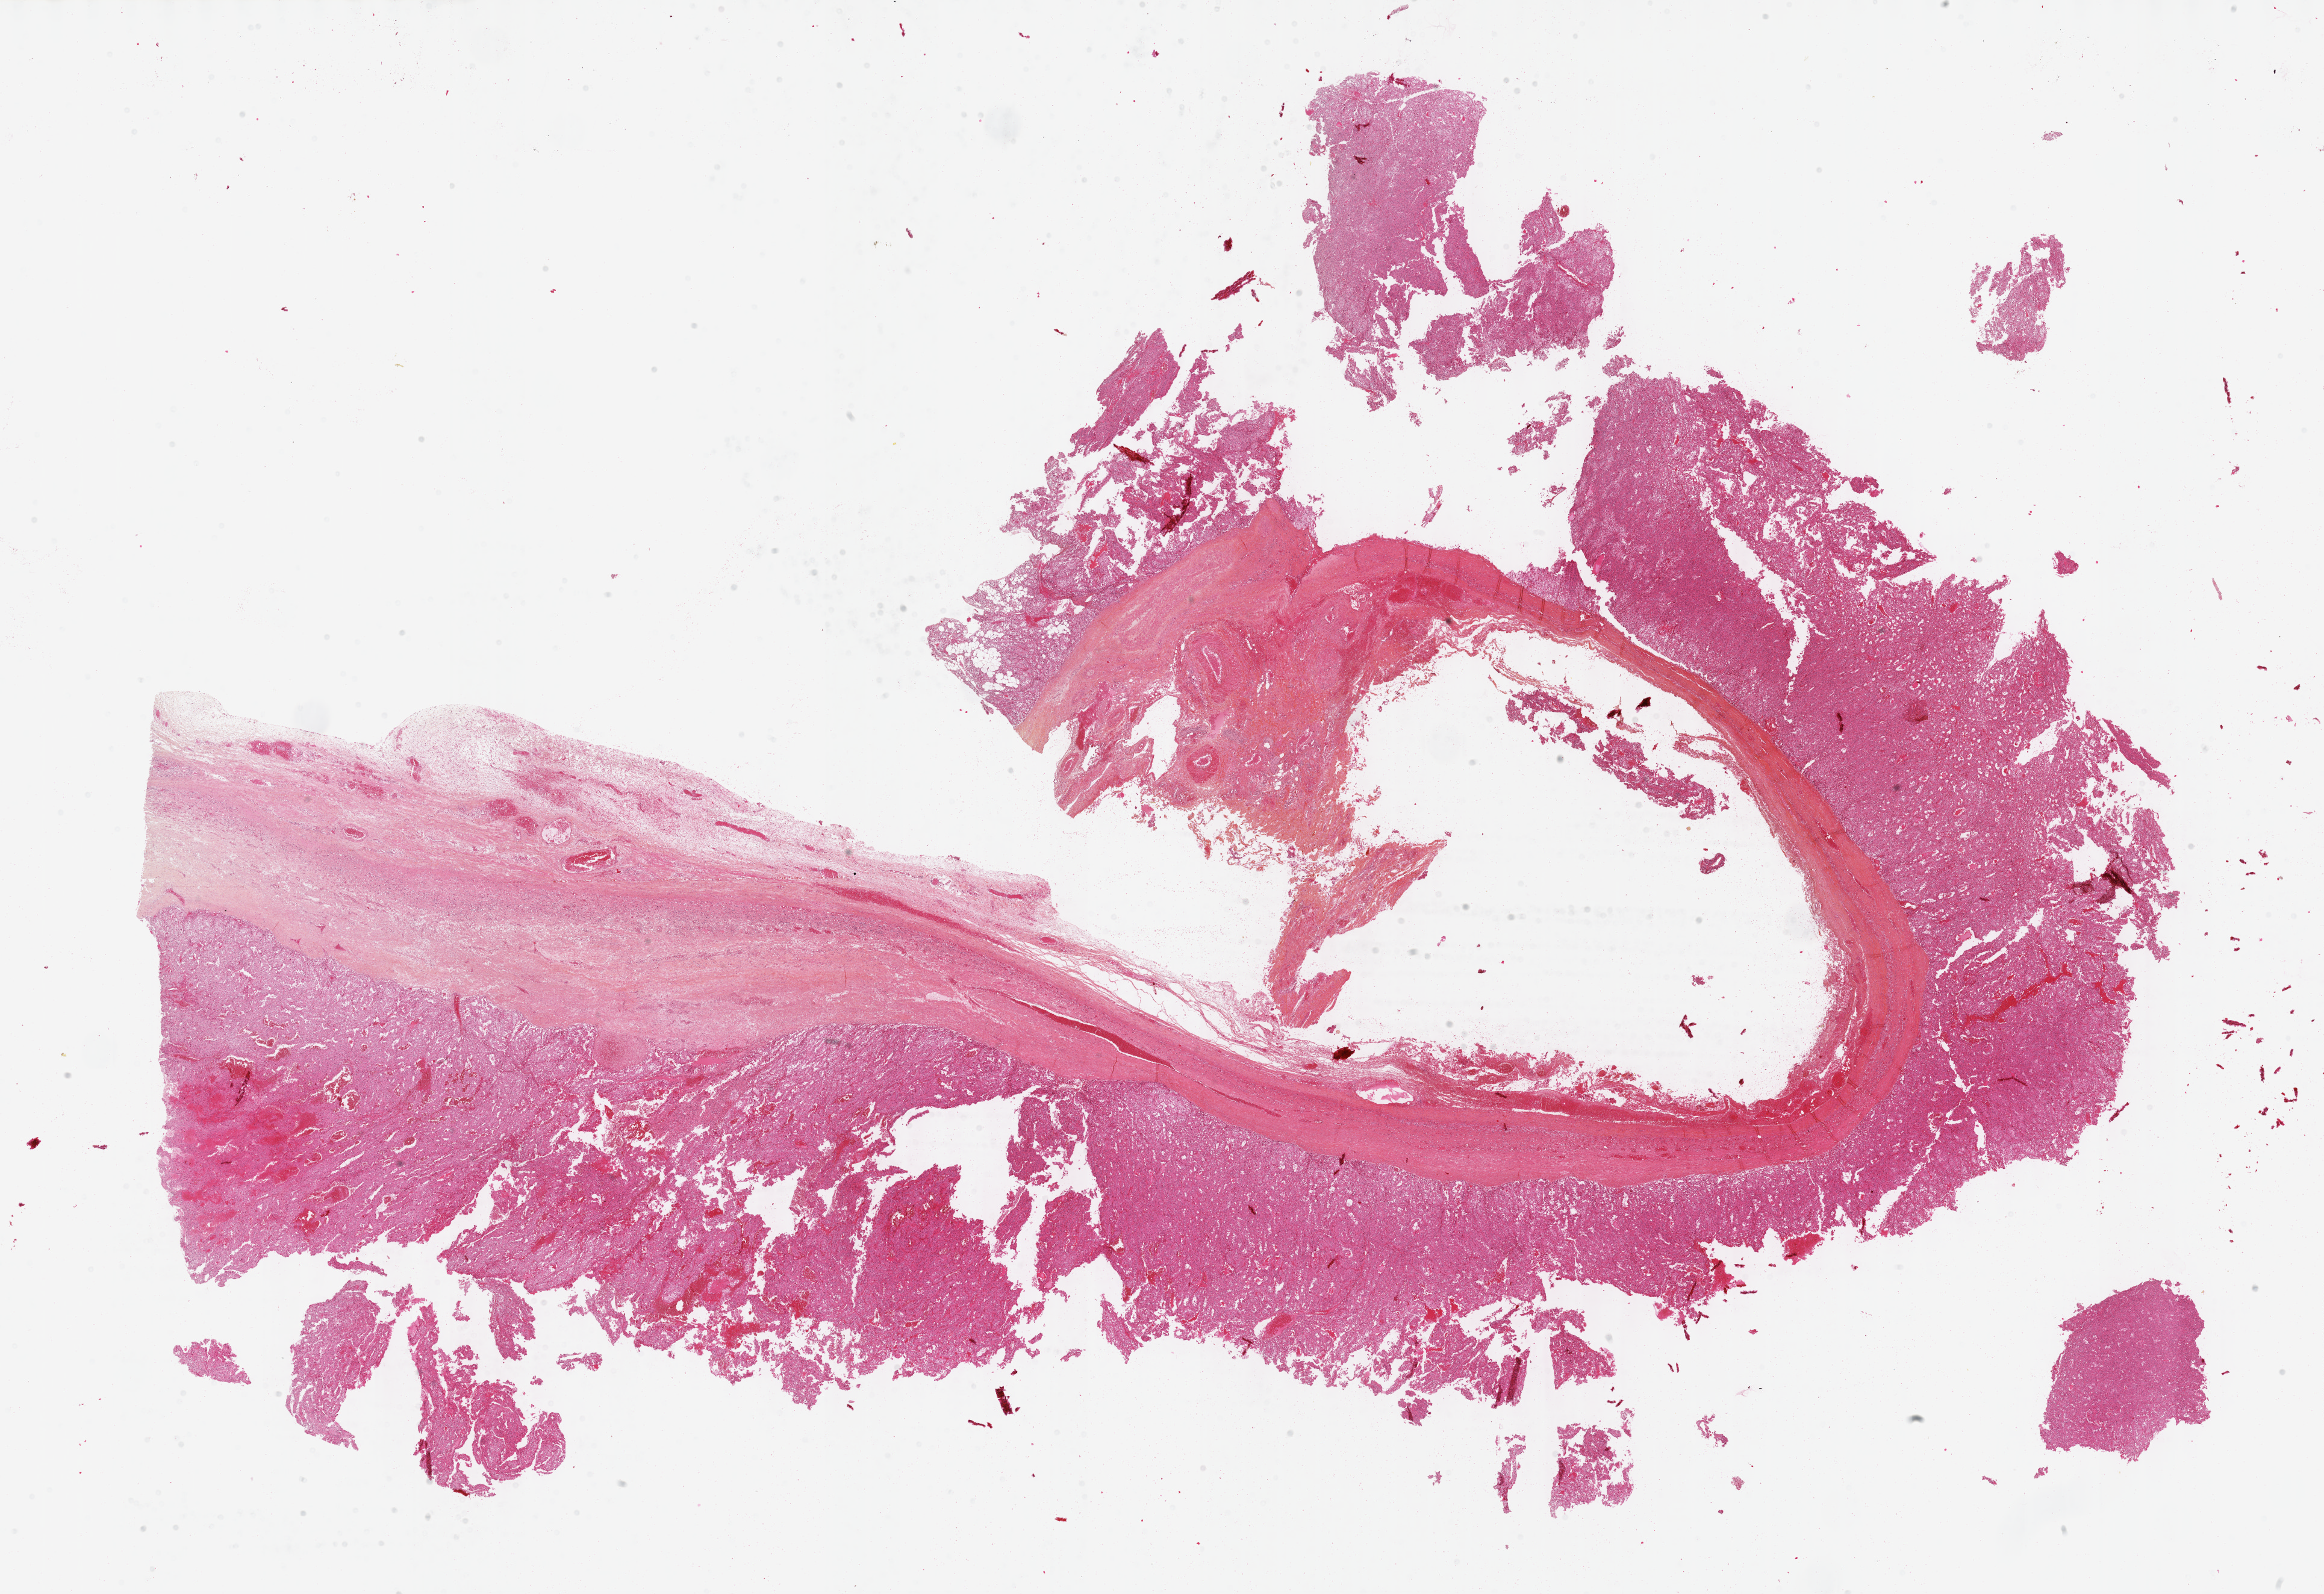
Whole-slide histology image, H&E — low-resolution overview of the scanned area, about 31.2 x 21.4 mm, formalin-fixed paraffin-embedded (FFPE) diagnostic section, adrenal cortex, primary tumour sample. Patient: female, age at initial diagnosis 34 years.
• diagnosis: Adrenal cortical carcinoma (cortex of adrenal gland)